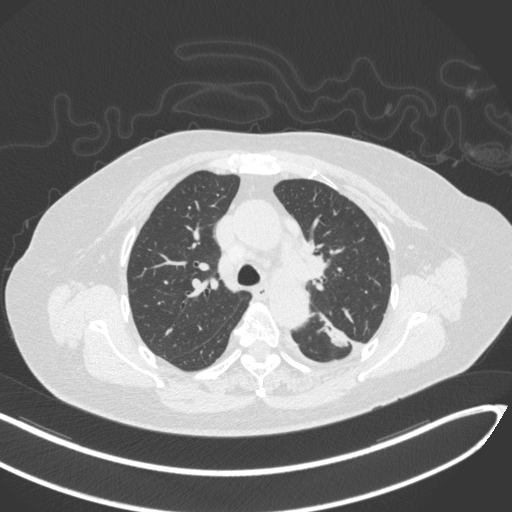
Chest CT, one axial slice; position 217 of 270 along the scan axis; reconstruction kernel B31f; lung window (W 1500 / L -600 HU); 512 × 512 image matrix. Patient: female, 76 years. Case-level facts recorded for this patient, not image findings: clinical TNM (as recorded): T1c N0 M0.
Structures marked on this image (rectangle marked by the reading radiologist):
- lung tumour (recorded histology: adenocarcinoma): box from (x=312, y=307) to (x=355, y=353) px